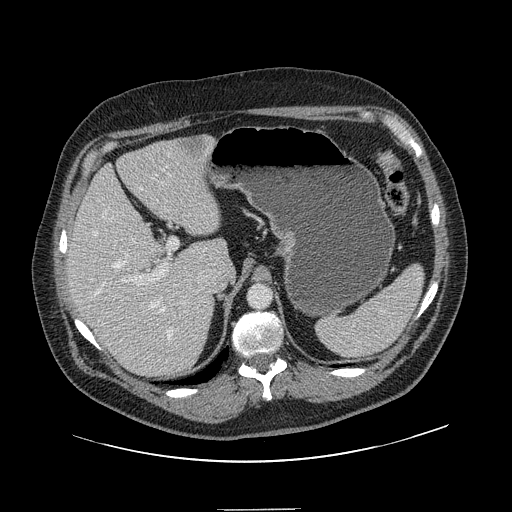
Contrast-enhanced abdominal CT, one axial slice. Position 99 of 154 along the scan axis. Intravenous contrast given. Soft-tissue window (W 400 / L 40 HU). 2.5 mm slice thickness. 512 × 512 image matrix, field of view 451 × 451 mm. Male patient, age 61 years. Case-level facts recorded for this patient, not image findings: diagnosis: colorectal cancer liver metastases, imaged before liver resection; multiple liver metastases: yes; largest metastasis: 2.6 cm.
Outlined on this slice (expert manual segmentation):
- hepatic veins: bounding box [x1, y1, x2, y2] px = [93, 210, 174, 339]
- liver: [68, 137, 225, 379]
- planned liver remnant (the part of the liver to remain after resection): [68, 145, 226, 362]
- portal vein (with intrahepatic branches): [108, 168, 186, 305]
- liver metastasis: [183, 139, 212, 157]